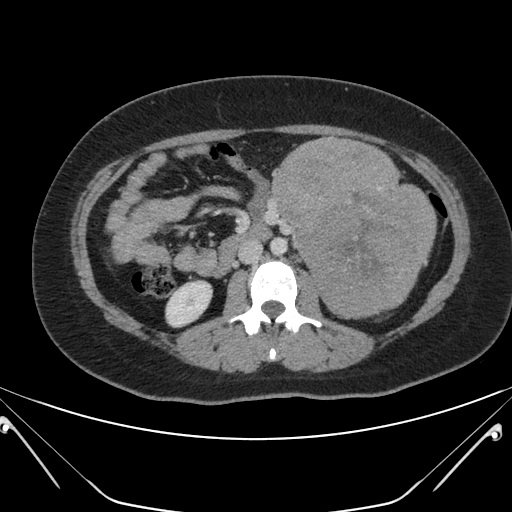
Contrast-enhanced abdominal CT, one axial slice. Position 102 of 168 along the scan axis. 120 kVp. Intravenous contrast given. Soft-tissue window (W 400 / L 40 HU). 512 × 512 image matrix, field of view 394 × 394 mm. Patient: female, 26 years. Case-level facts recorded for this patient, not image findings: diagnosis: adrenocortical carcinoma; tumour side: left adrenal; tumour size at pathology: 28 cm; Ki-67 index: 20 %; stage (as recorded): 2.
Annotated regions visible in this slice (semi-automatic segmentation, software-assisted and operator-edited):
- mass: box from (x=274, y=137) to (x=436, y=317) px